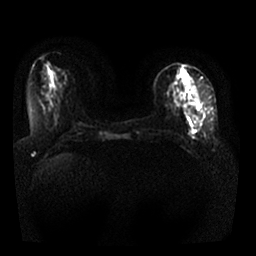
Breast MRI, one axial slice; position 9 of 25 along the scan axis; diffusion-weighted series; image 2 of 4 stored at this slice position (different b-values; order by instance number); 1.5 T; 256 × 256 image matrix. Female patient.
Structures marked on this image (manually delineated by an expert):
- tumour on diffusion-weighted imaging: box from (x=197, y=103) to (x=200, y=110) px